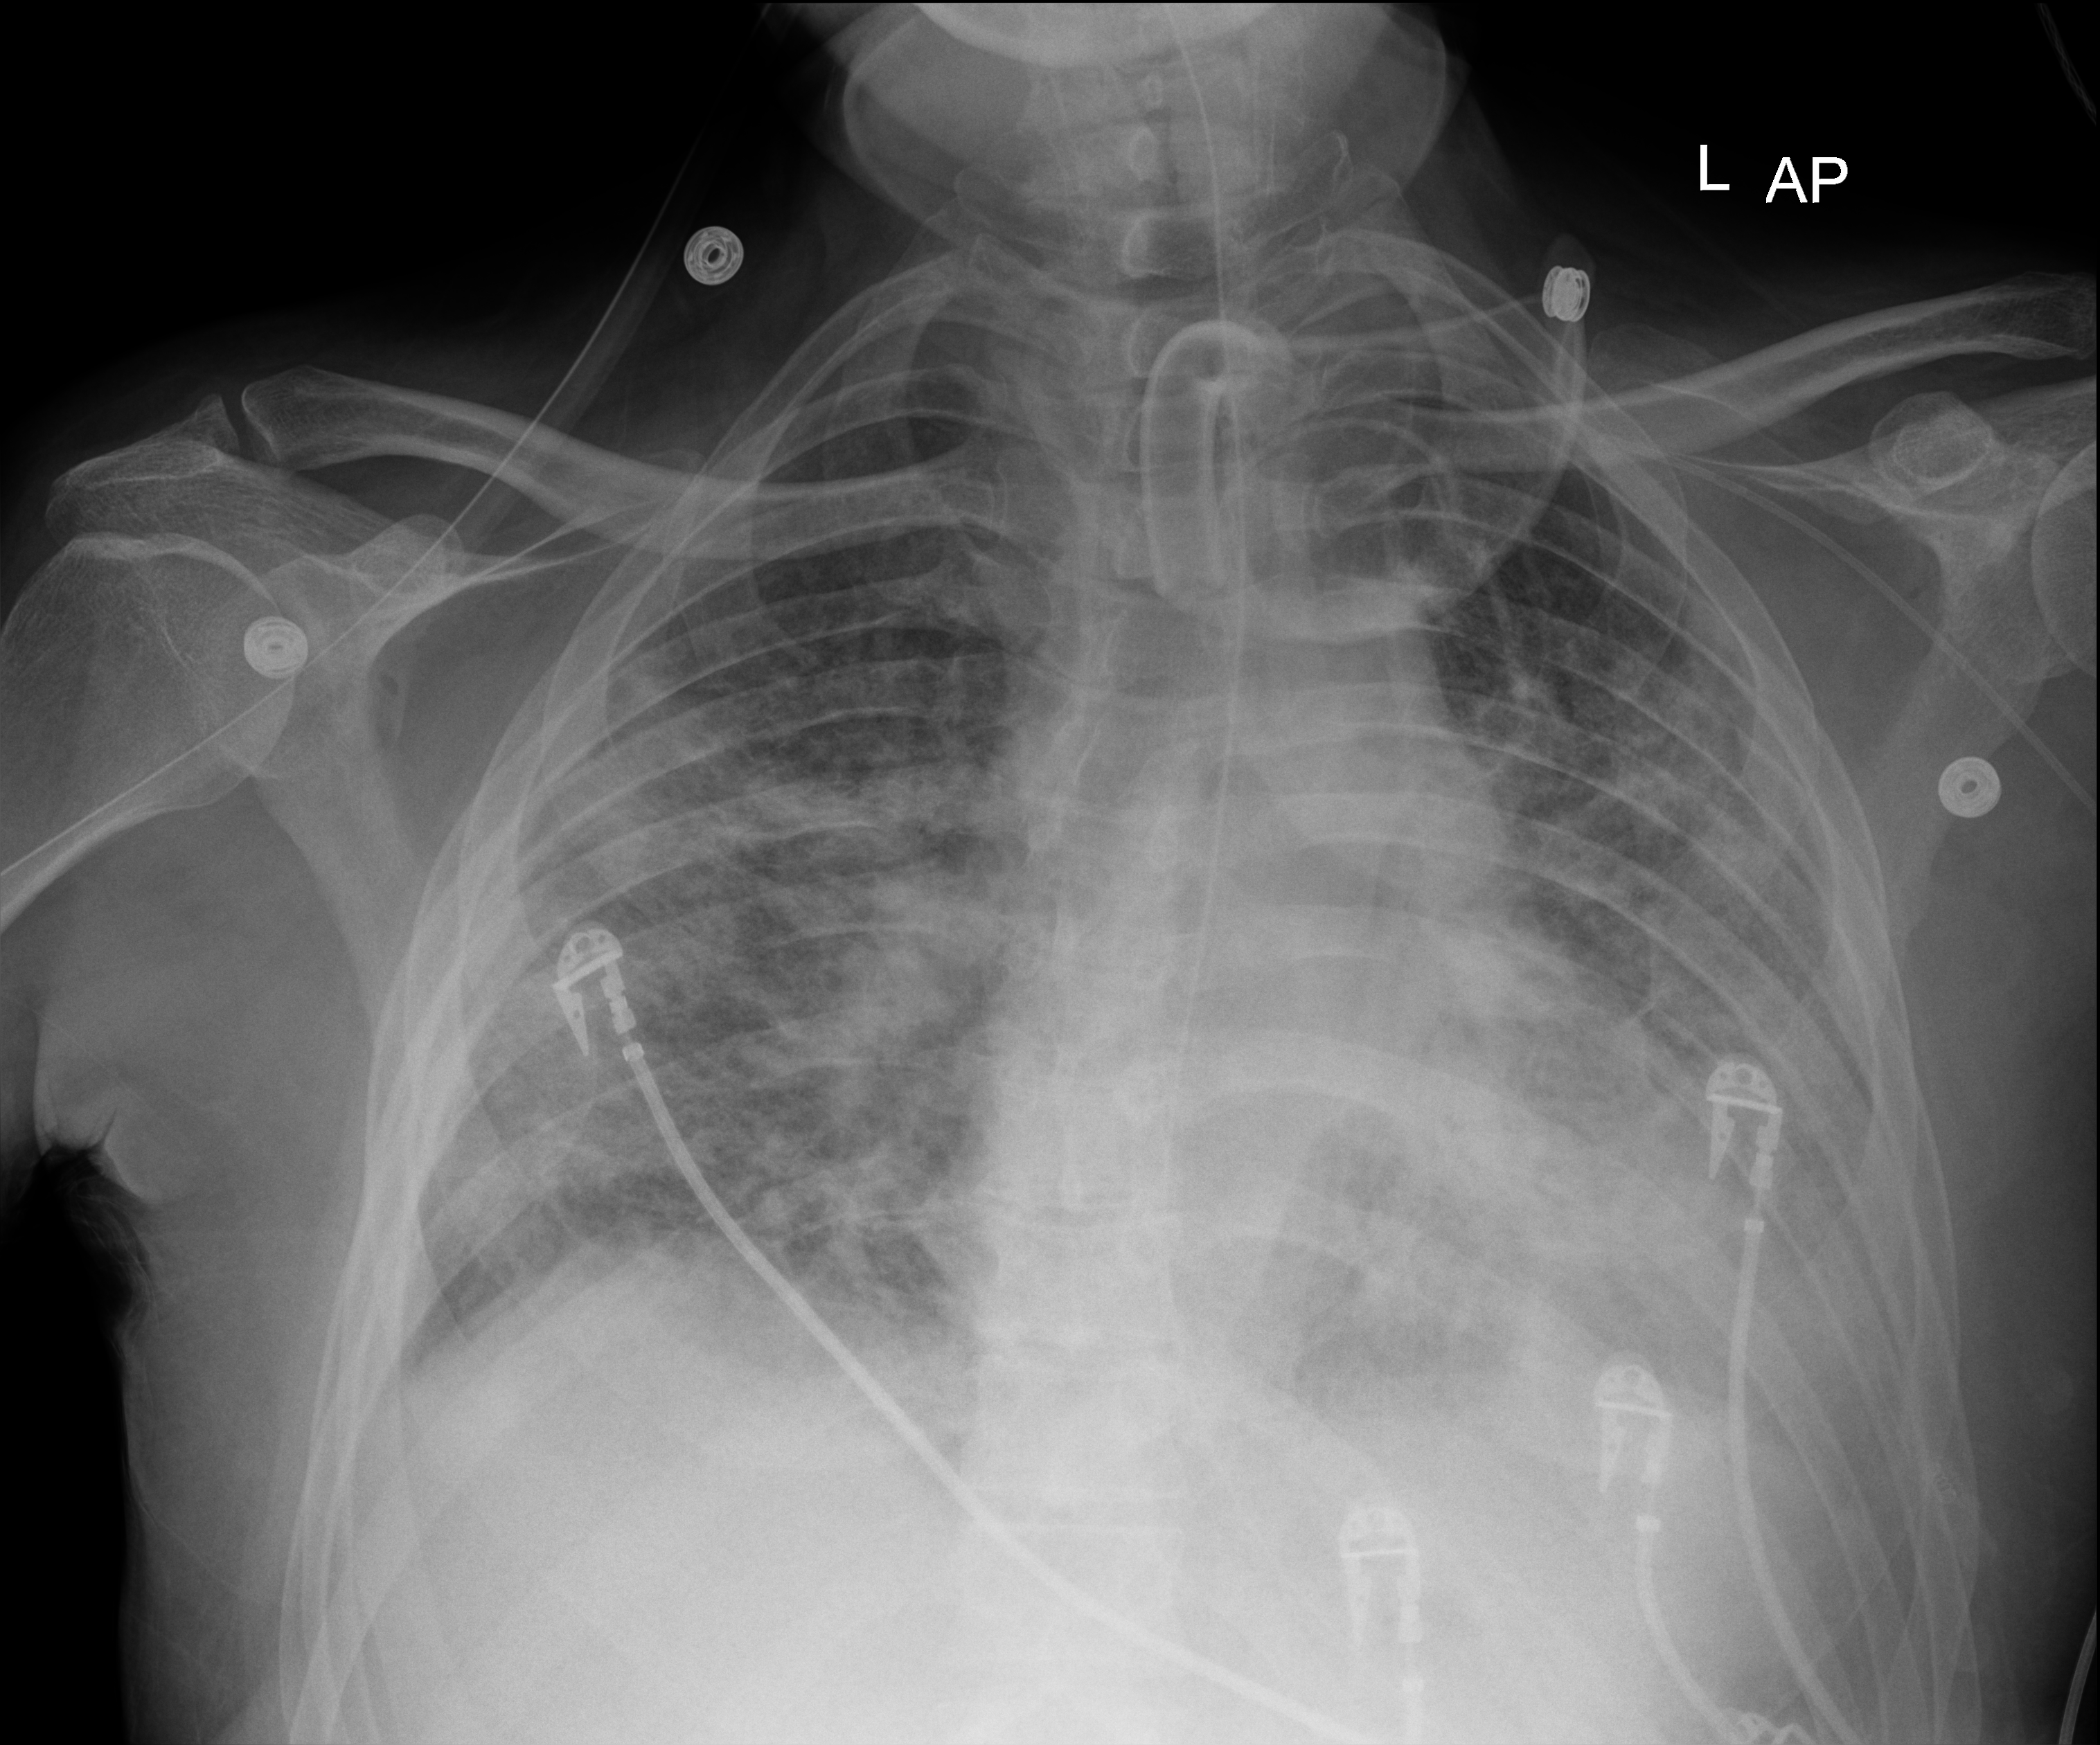
Chest radiograph, anteroposterior (AP) projection. Male patient hospitalised with COVID-19, age 18–59 years.
From the hospital-stay record, not from the radiograph (when in the stay this image was taken is not recorded):
- mechanically ventilated during this hospital stay: yes
- admitted to intensive care during this hospital stay: yes